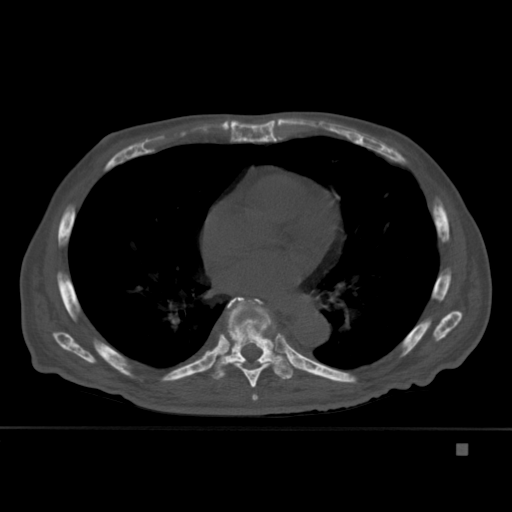
CT including the spine, one axial slice; position 271 of 451 along the scan axis; bone window (W 1800 / L 400 HU); 1.5 mm slice thickness; 512 × 512 image matrix, field of view 378 × 378 mm. Male patient, age 75 years. From the clinical record (not read from this slice): primary cancer: prostate.
Annotated regions visible in this slice (semi-automatically segmented with operator editing):
- T6 vertebra: box from (x=252, y=394) to (x=258, y=401) px
- T7 vertebra: (x=229, y=298)–(x=277, y=388)
- T8 vertebra: (x=207, y=297)–(x=293, y=380)